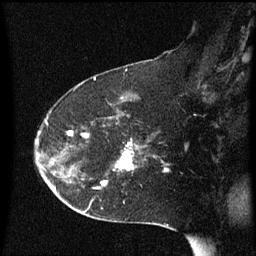
Breast MRI (dynamic contrast-enhanced), one sagittal slice. Dynamic contrast-enhanced series, image 2 of 3 at this slice position (ordered by acquisition). 1.5 T. TE 4.2 ms, TR 8.4 ms. 2 mm slice thickness. 256 × 256 image matrix, field of view 200 × 200 mm. Female patient, age 54 years. Case-level facts recorded for this patient, not image findings: setting: breast cancer imaged before/during neoadjuvant chemotherapy; receptor status: HR-positive, HER2-negative.
Structures marked on this image (semi-automatically segmented with operator editing):
- analysis volume of interest (the breast-tissue region the enhancement analysis was run in; not a lesion): box from (x=101, y=126) to (x=170, y=187) px
- tumour enhancement mask (voxels above the 70 % enhancement threshold inside the analysis volume of interest): (x=103, y=144)–(x=134, y=185)